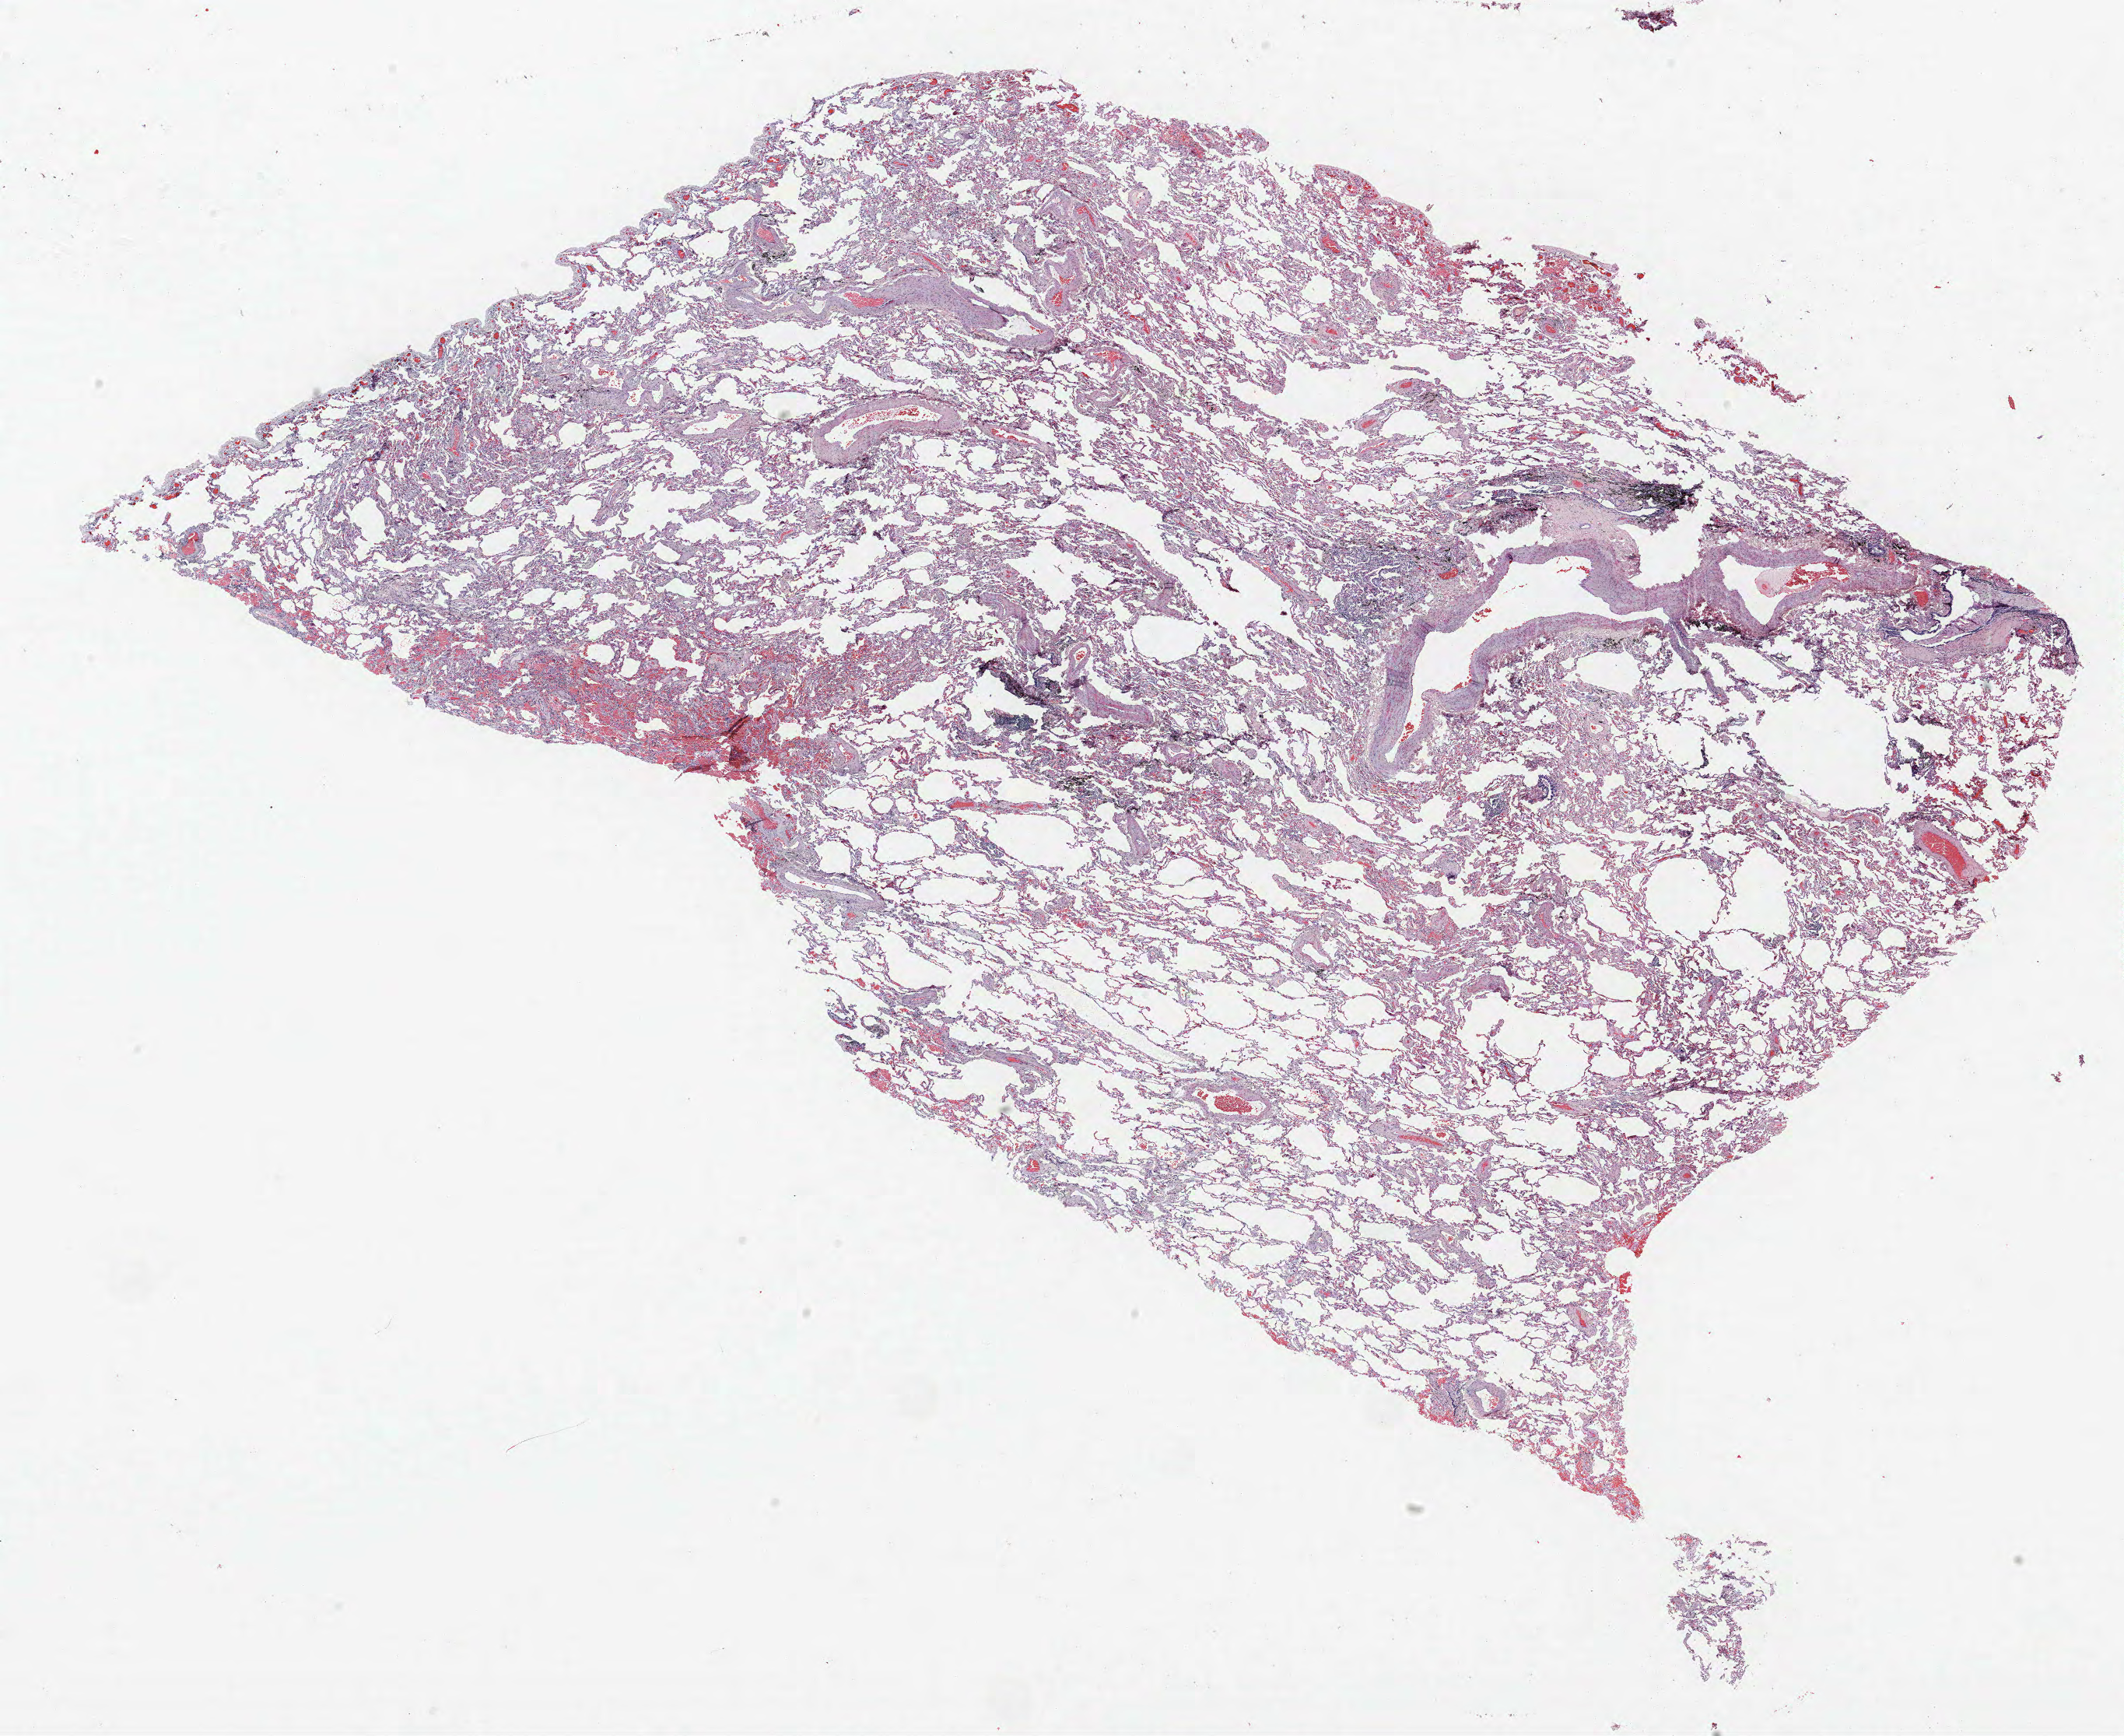
Whole-slide histology image, H&E — shown as a low-resolution overview of the whole scanned area (about 21.8 x 17.9 mm, slide scanned at 40x), FFPE section, lung tissue. Male patient, aged 72 at enrolment. Former smoker at enrolment. Grade: poorly differentiated (G3).
* primary tumour location (clinical record): right upper lobe
* tumour size (pathology): 30 mm
* participant's lung-cancer diagnosis: Squamous cell carcinoma, NOS (ICD-O-3 8070/3)
* stage (AJCC 6th edition): IA